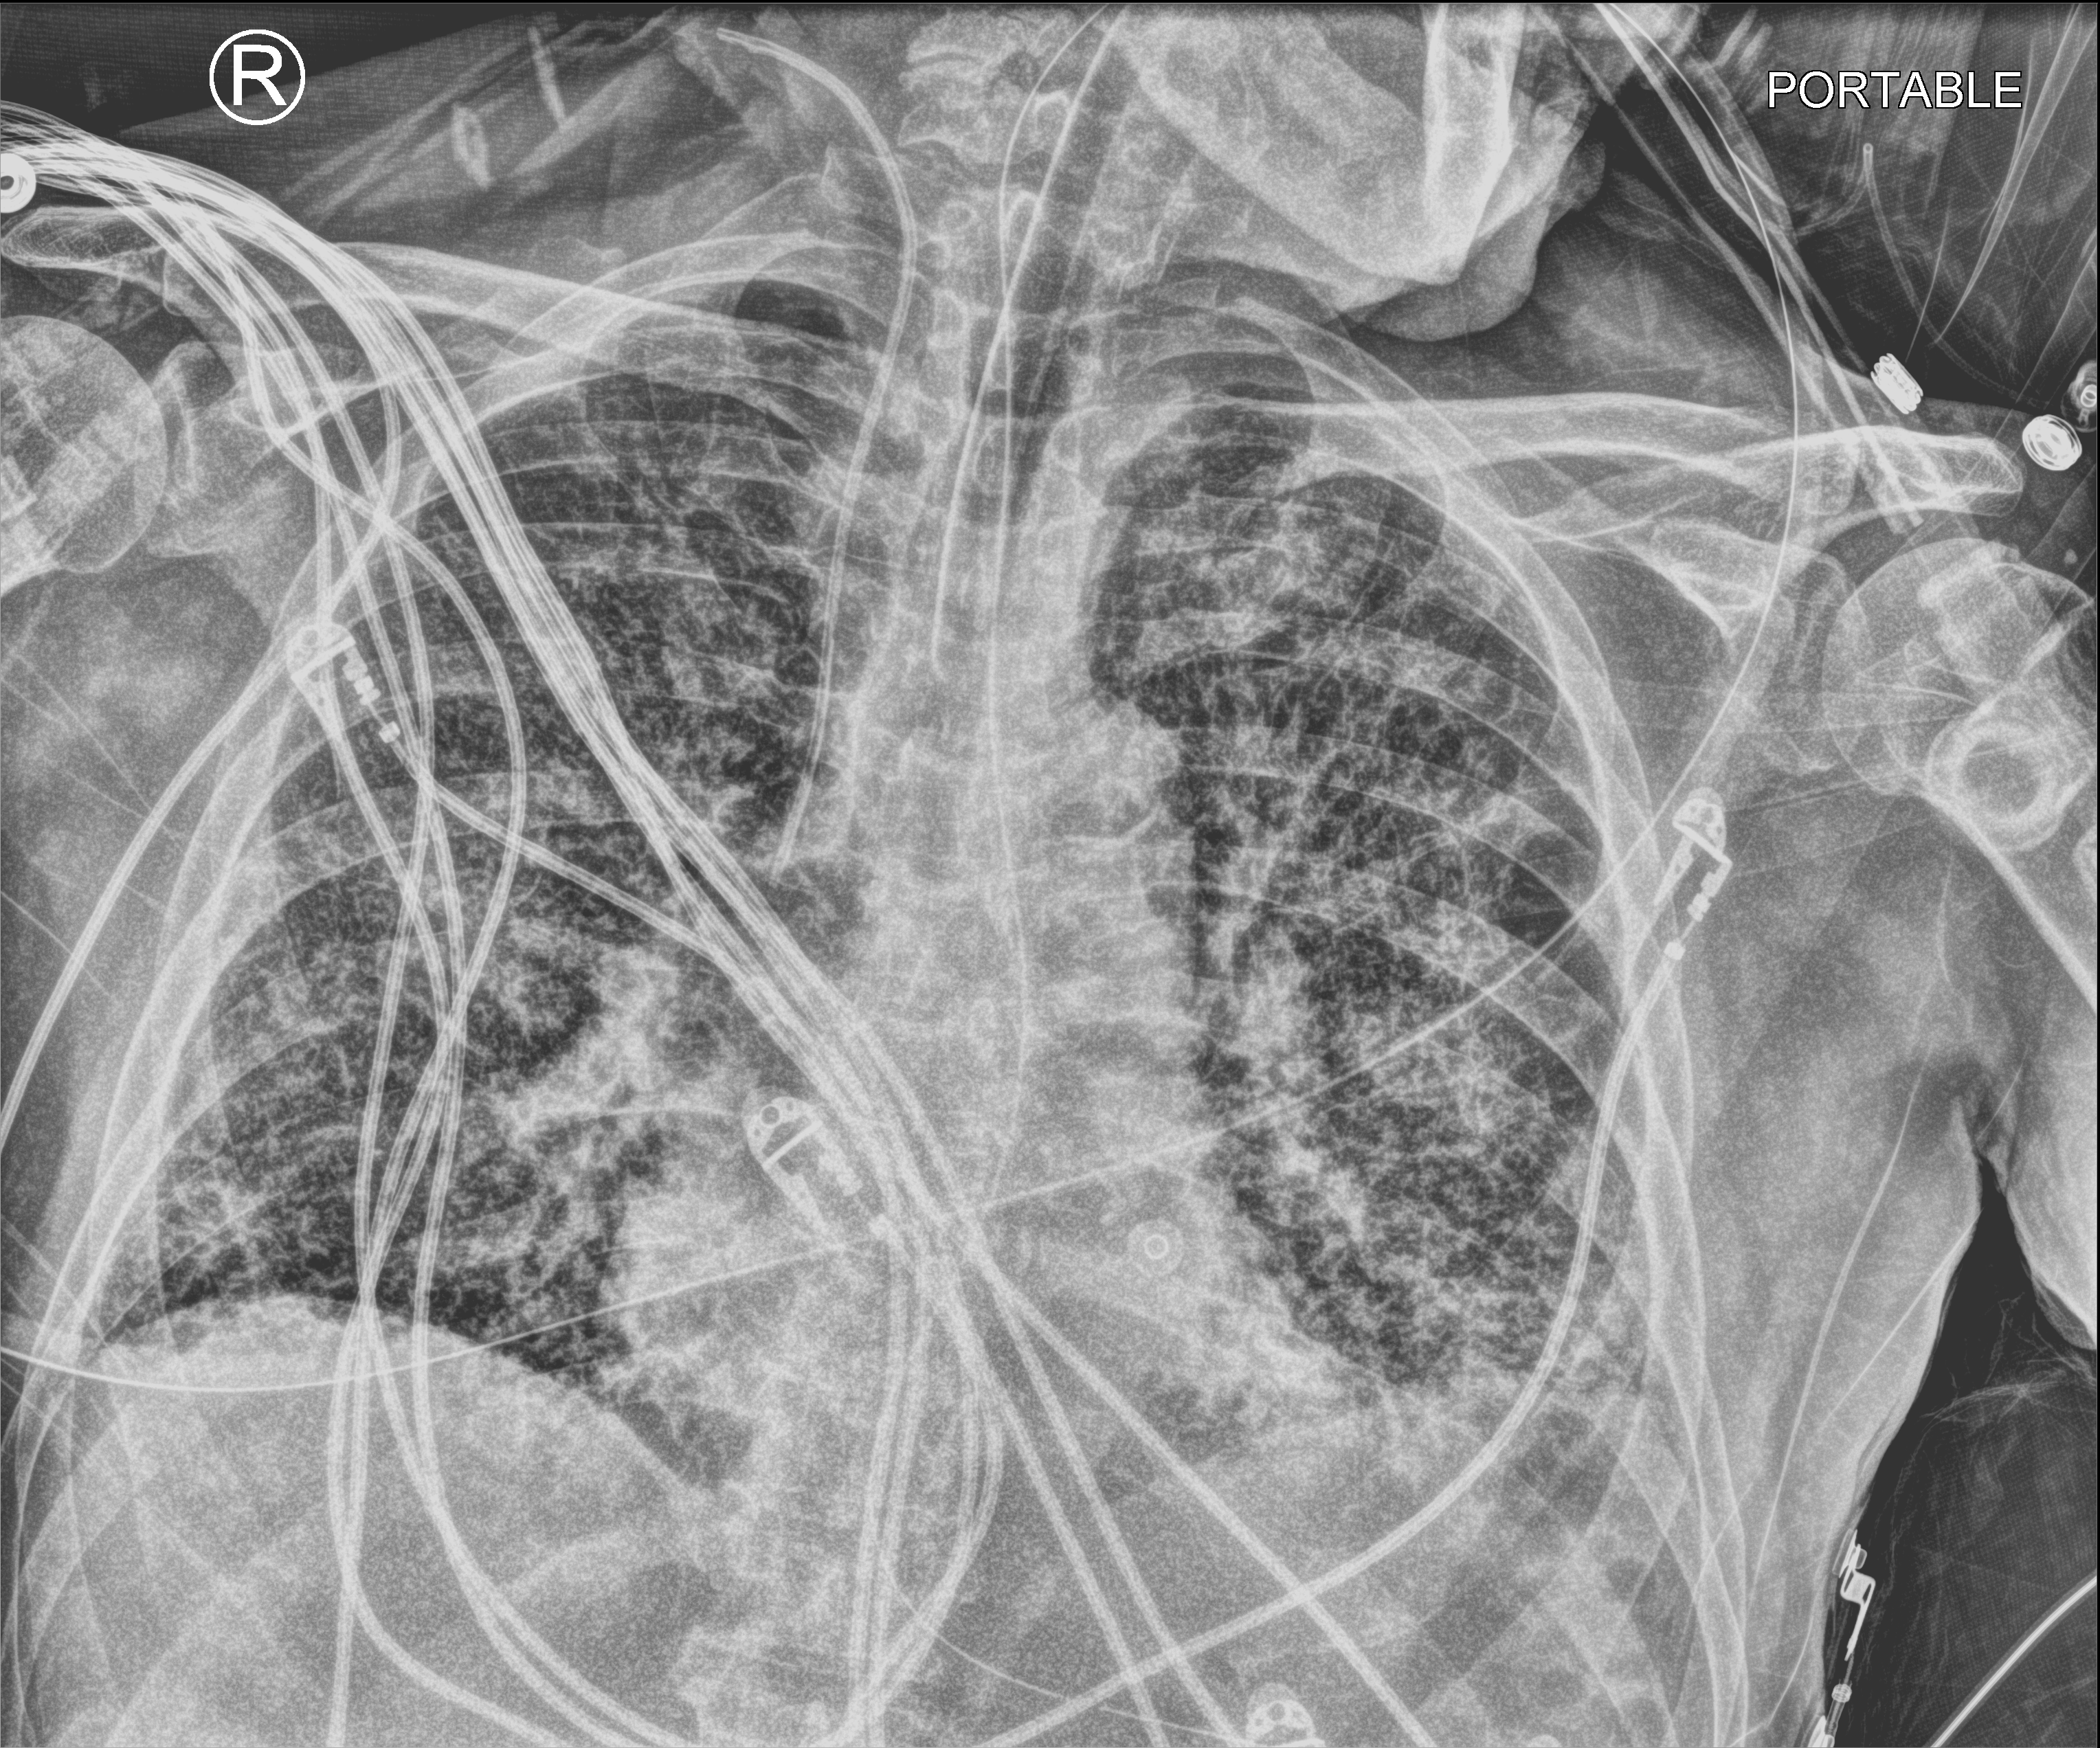
Portable chest radiograph, anteroposterior (AP) projection. Male patient hospitalised with COVID-19, age 75–90 years.
From the hospital-stay record, not from the radiograph (when in the stay this image was taken is not recorded):
- hypertension (admission record): yes